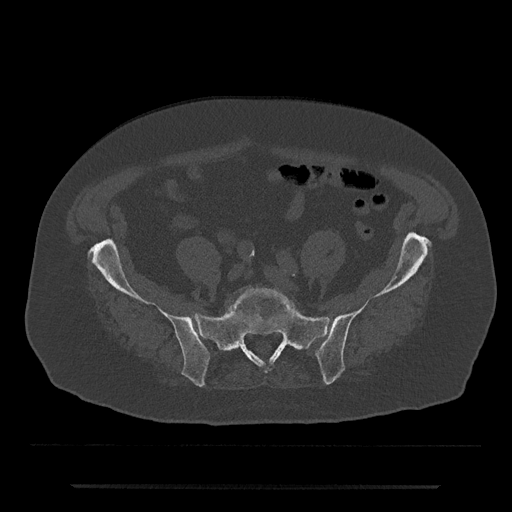
CT including the spine, one axial slice; reconstruction kernel Br40s/3; bone window (W 1800 / L 400 HU); 0.5 mm slice thickness; 512 × 512 image matrix. Patient: male, 80 years. Case-level facts recorded for this patient, not image findings: primary cancer: prostate.
Outlined on this slice (semi-automatic segmentation, software-assisted and operator-edited):
- L5 vertebra: bounding box [x1, y1, x2, y2] px = [228, 287, 299, 316]